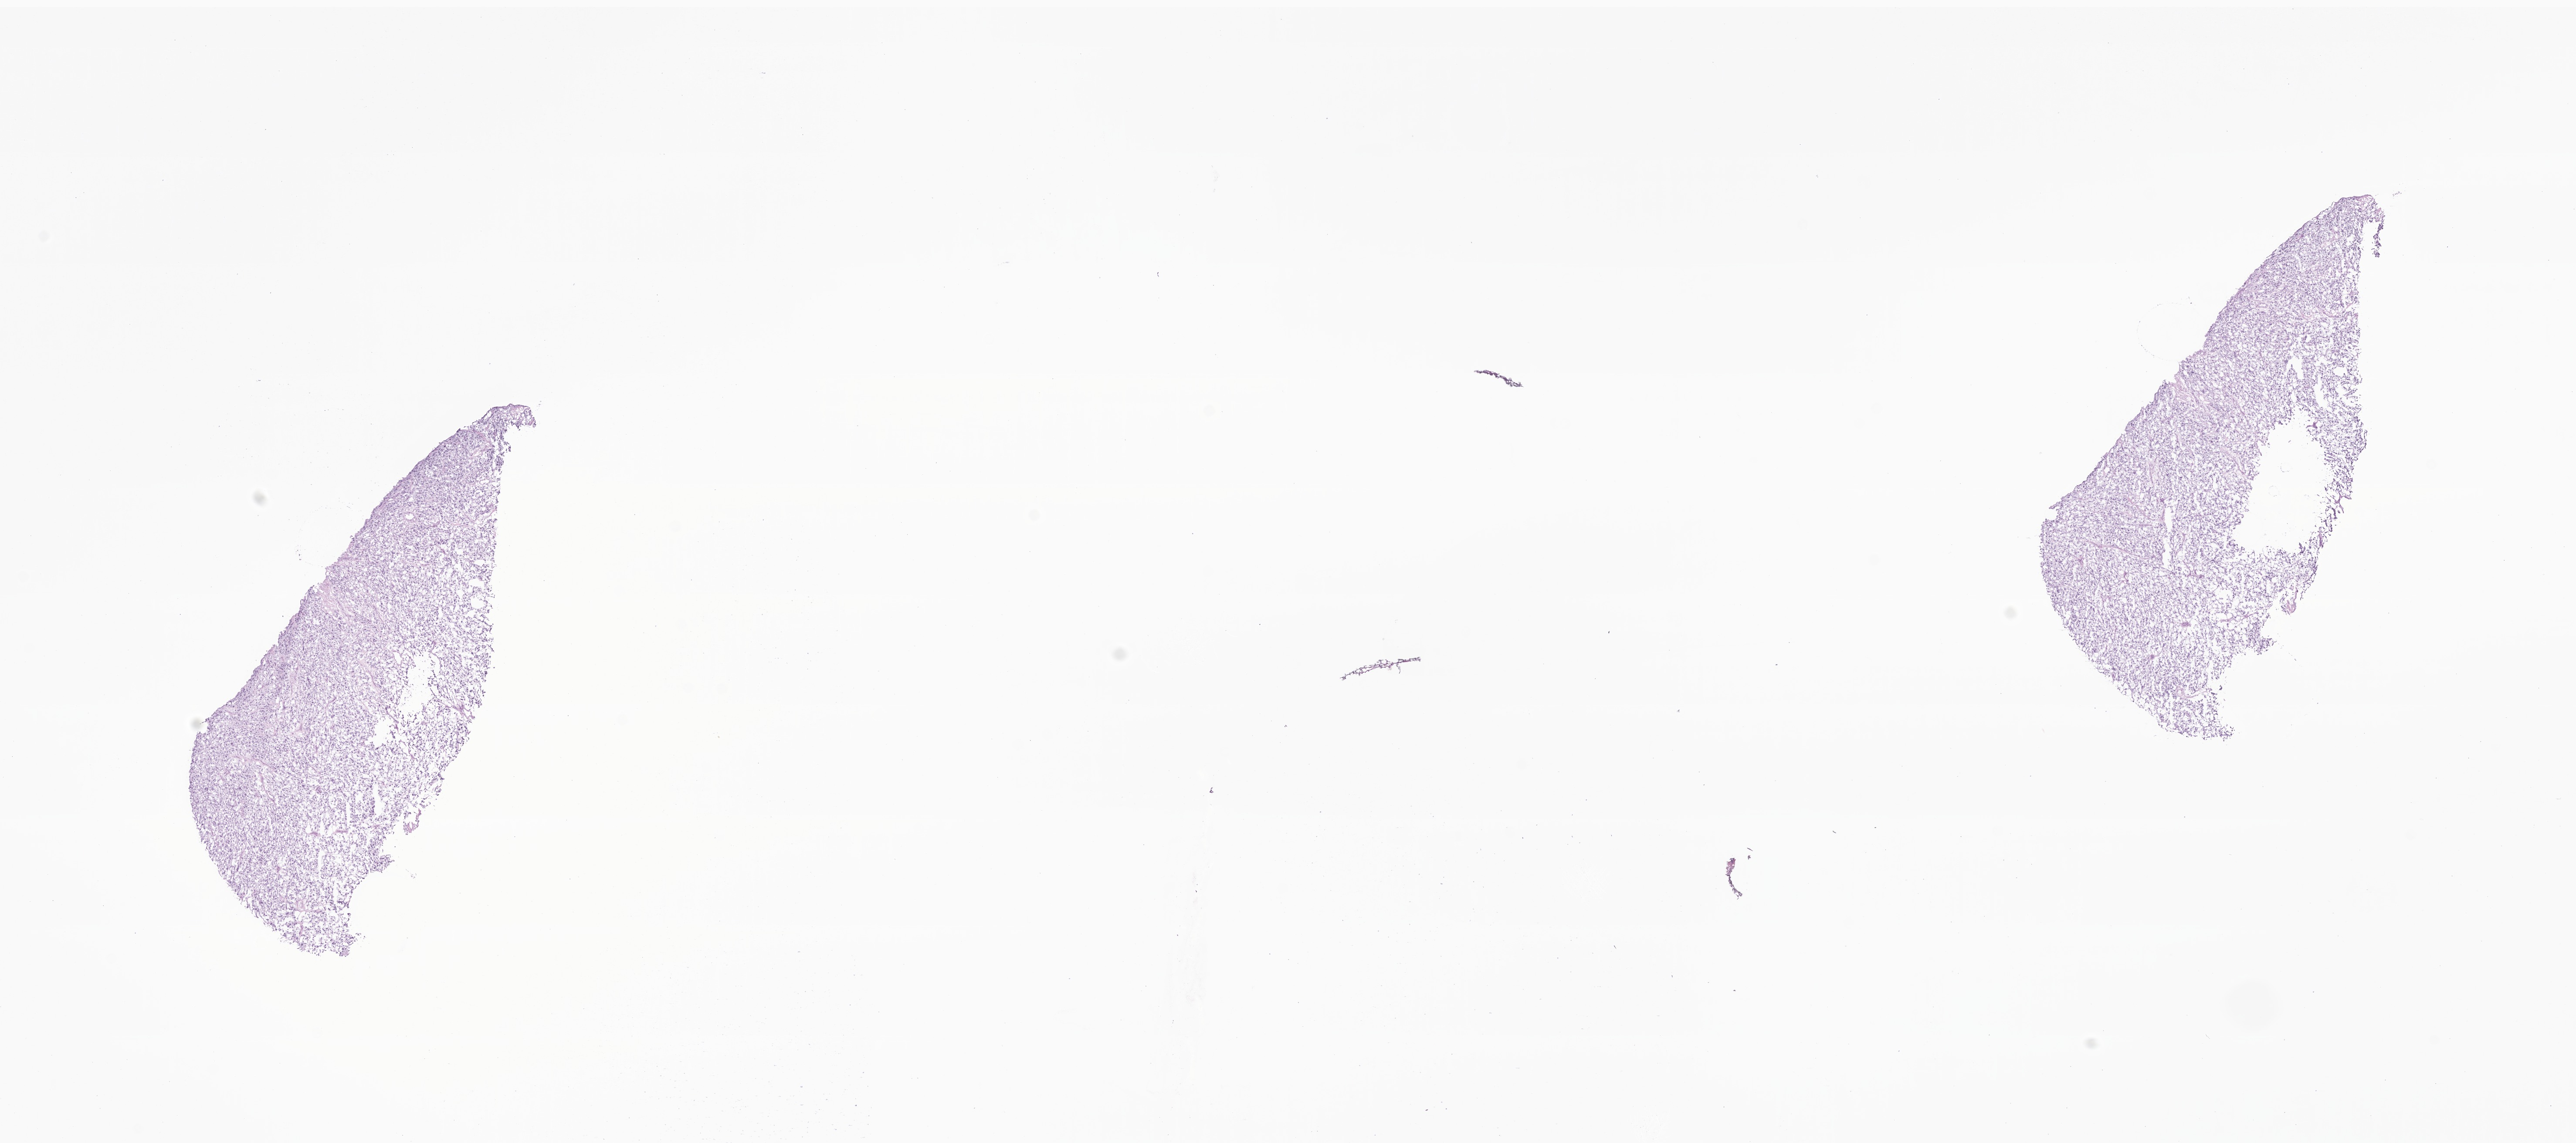
Digitized haematoxylin and eosin-stained section of tumor tissue from the thorax, whole scanned area (about 24.9 x 11.1 mm) shown as a low-resolution overview, cryosection (OCT / tissue freezing medium). Patient: male, age 796 days.
- diagnosis (ICD-O-3 morphology term): Rhabdomyosarcoma, NOS